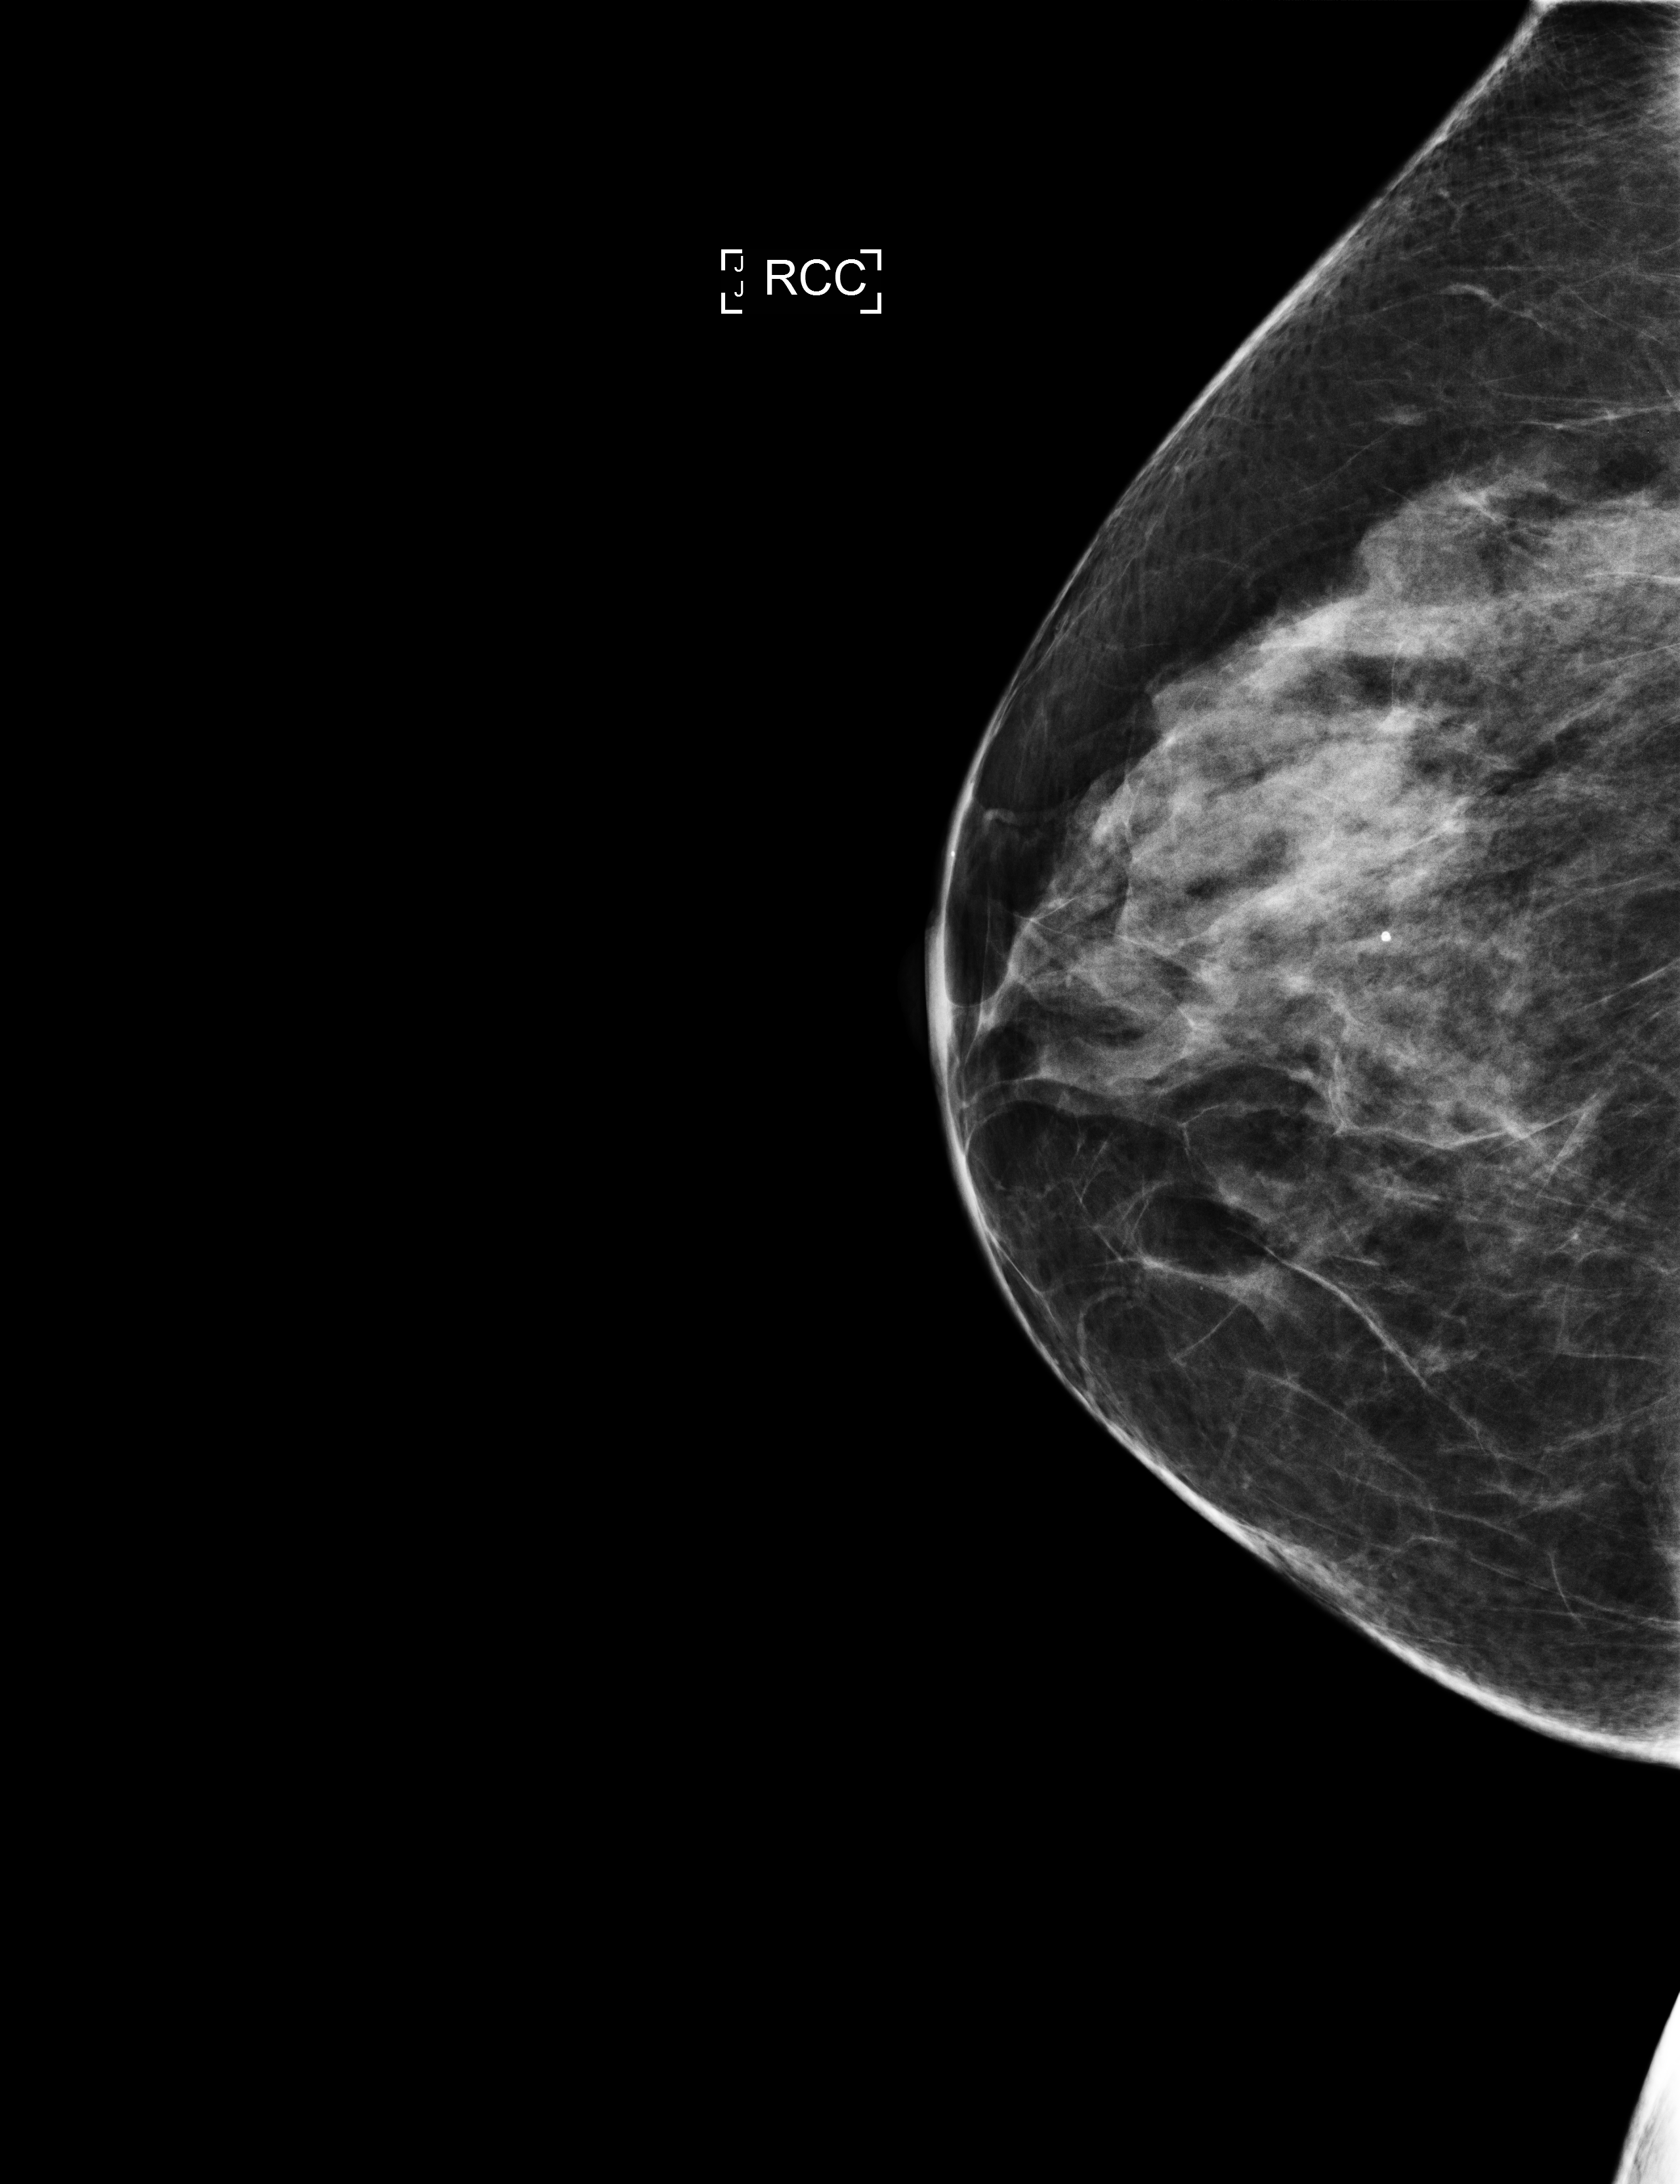
Full-field digital mammogram (FFDM), right breast, craniocaudal (CC) view, annual screening mammography examination, compressed breast thickness 88 mm. Patient aged 66 years (female).
Final BI-RADS assessment for this screening round (tomosynthesis exam, both breasts): category 2.